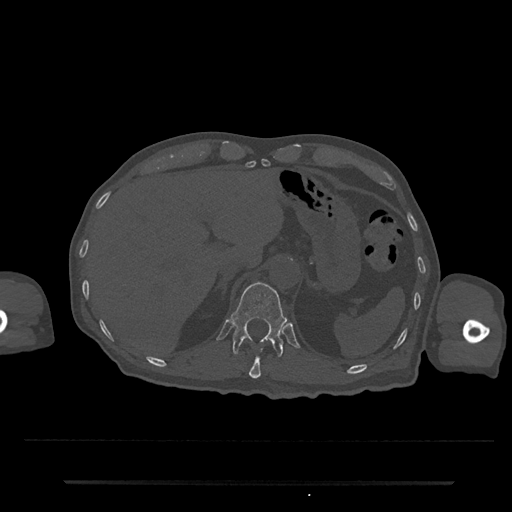
CT including the spine, one axial slice; slice 214 of 797 in the series (ordered by position); reconstruction kernel Br40s/3; 120 kVp; bone window (W 1800 / L 400 HU); 0.5 mm slice thickness; 512 × 512 image matrix, field of view 427 × 427 mm. Male patient, age 74 years. From the clinical record (not read from this slice): primary cancer: prostate.
Structures marked on this image (semi-automatic segmentation, software-assisted and operator-edited):
- T11 vertebra: bounding box [x1, y1, x2, y2] px = [249, 348, 263, 379]
- T12 vertebra: [231, 282, 288, 357]